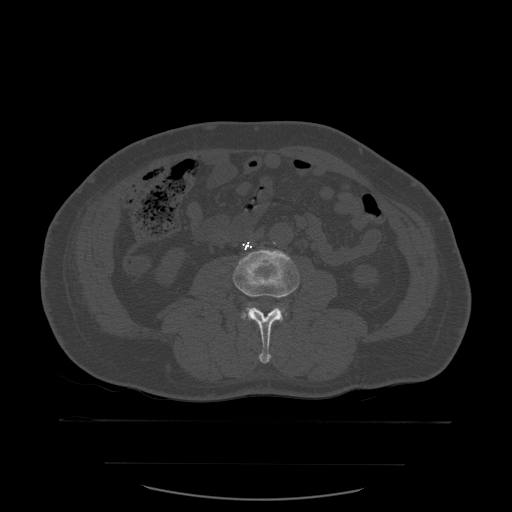
CT including the spine, one axial slice; slice 186 of 590 in the series (ordered by position); bone window (W 1800 / L 400 HU); 1.25 mm slice thickness; 512 × 512 image matrix, field of view 479 × 479 mm. Patient age 71 years. Case-level facts recorded for this patient, not image findings: primary cancer: lung.
Annotated regions visible in this slice (semi-automatic segmentation, software-assisted and operator-edited):
- L3 vertebra: box from (x=233, y=249) to (x=300, y=364) px
- L4 vertebra: (x=242, y=305)–(x=285, y=319)